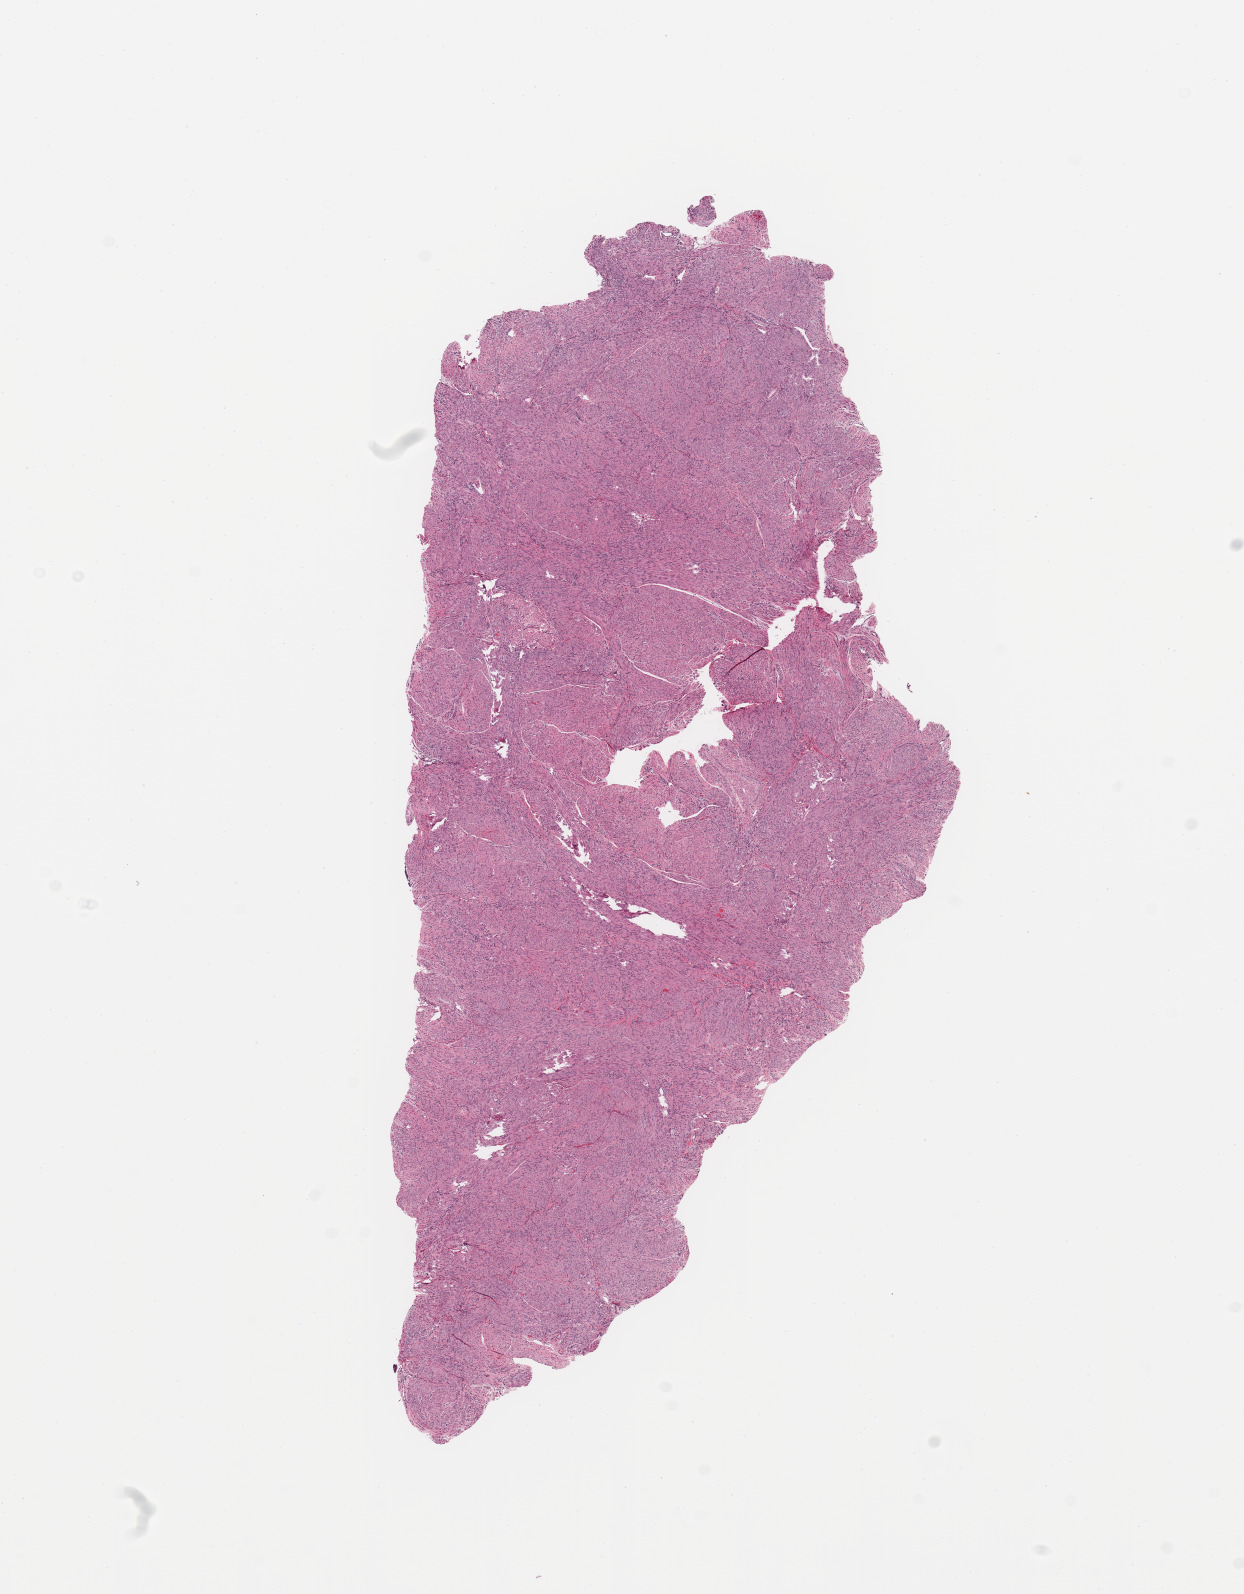
Whole-slide histology image, H&E-stained — low-resolution overview of the scanned area, about 9.8 x 12.6 mm; normal (non-tumour) tissue sample, sampled site: uterus. Patient: female, age 56 years.
- this section: normal (non-tumour) tissue from the same patient
- patient diagnosis: Endometrioid adenocarcinoma, NOS